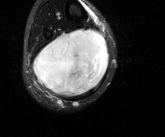
MRI of an extremity soft-tissue mass, one axial slice; position 49 of 81 along the scan axis; T2-weighted fat-saturated; MR volume resampled by the dataset authors to the PET/CT grid (not the native acquisition matrix); 165 × 137 image matrix, field of view 161 × 134 mm. Male patient. Case-level facts recorded for this patient, not image findings: histological type: liposarcoma - round cell; grade: high; site of the primary tumour: right calf.
Outlined on this slice (expert contour drawn on MRI and transferred to this co-registered scan by the dataset authors):
- gross tumour volume (mass): bounding box <34,27,109,97> (left, top, right, bottom; pixels)